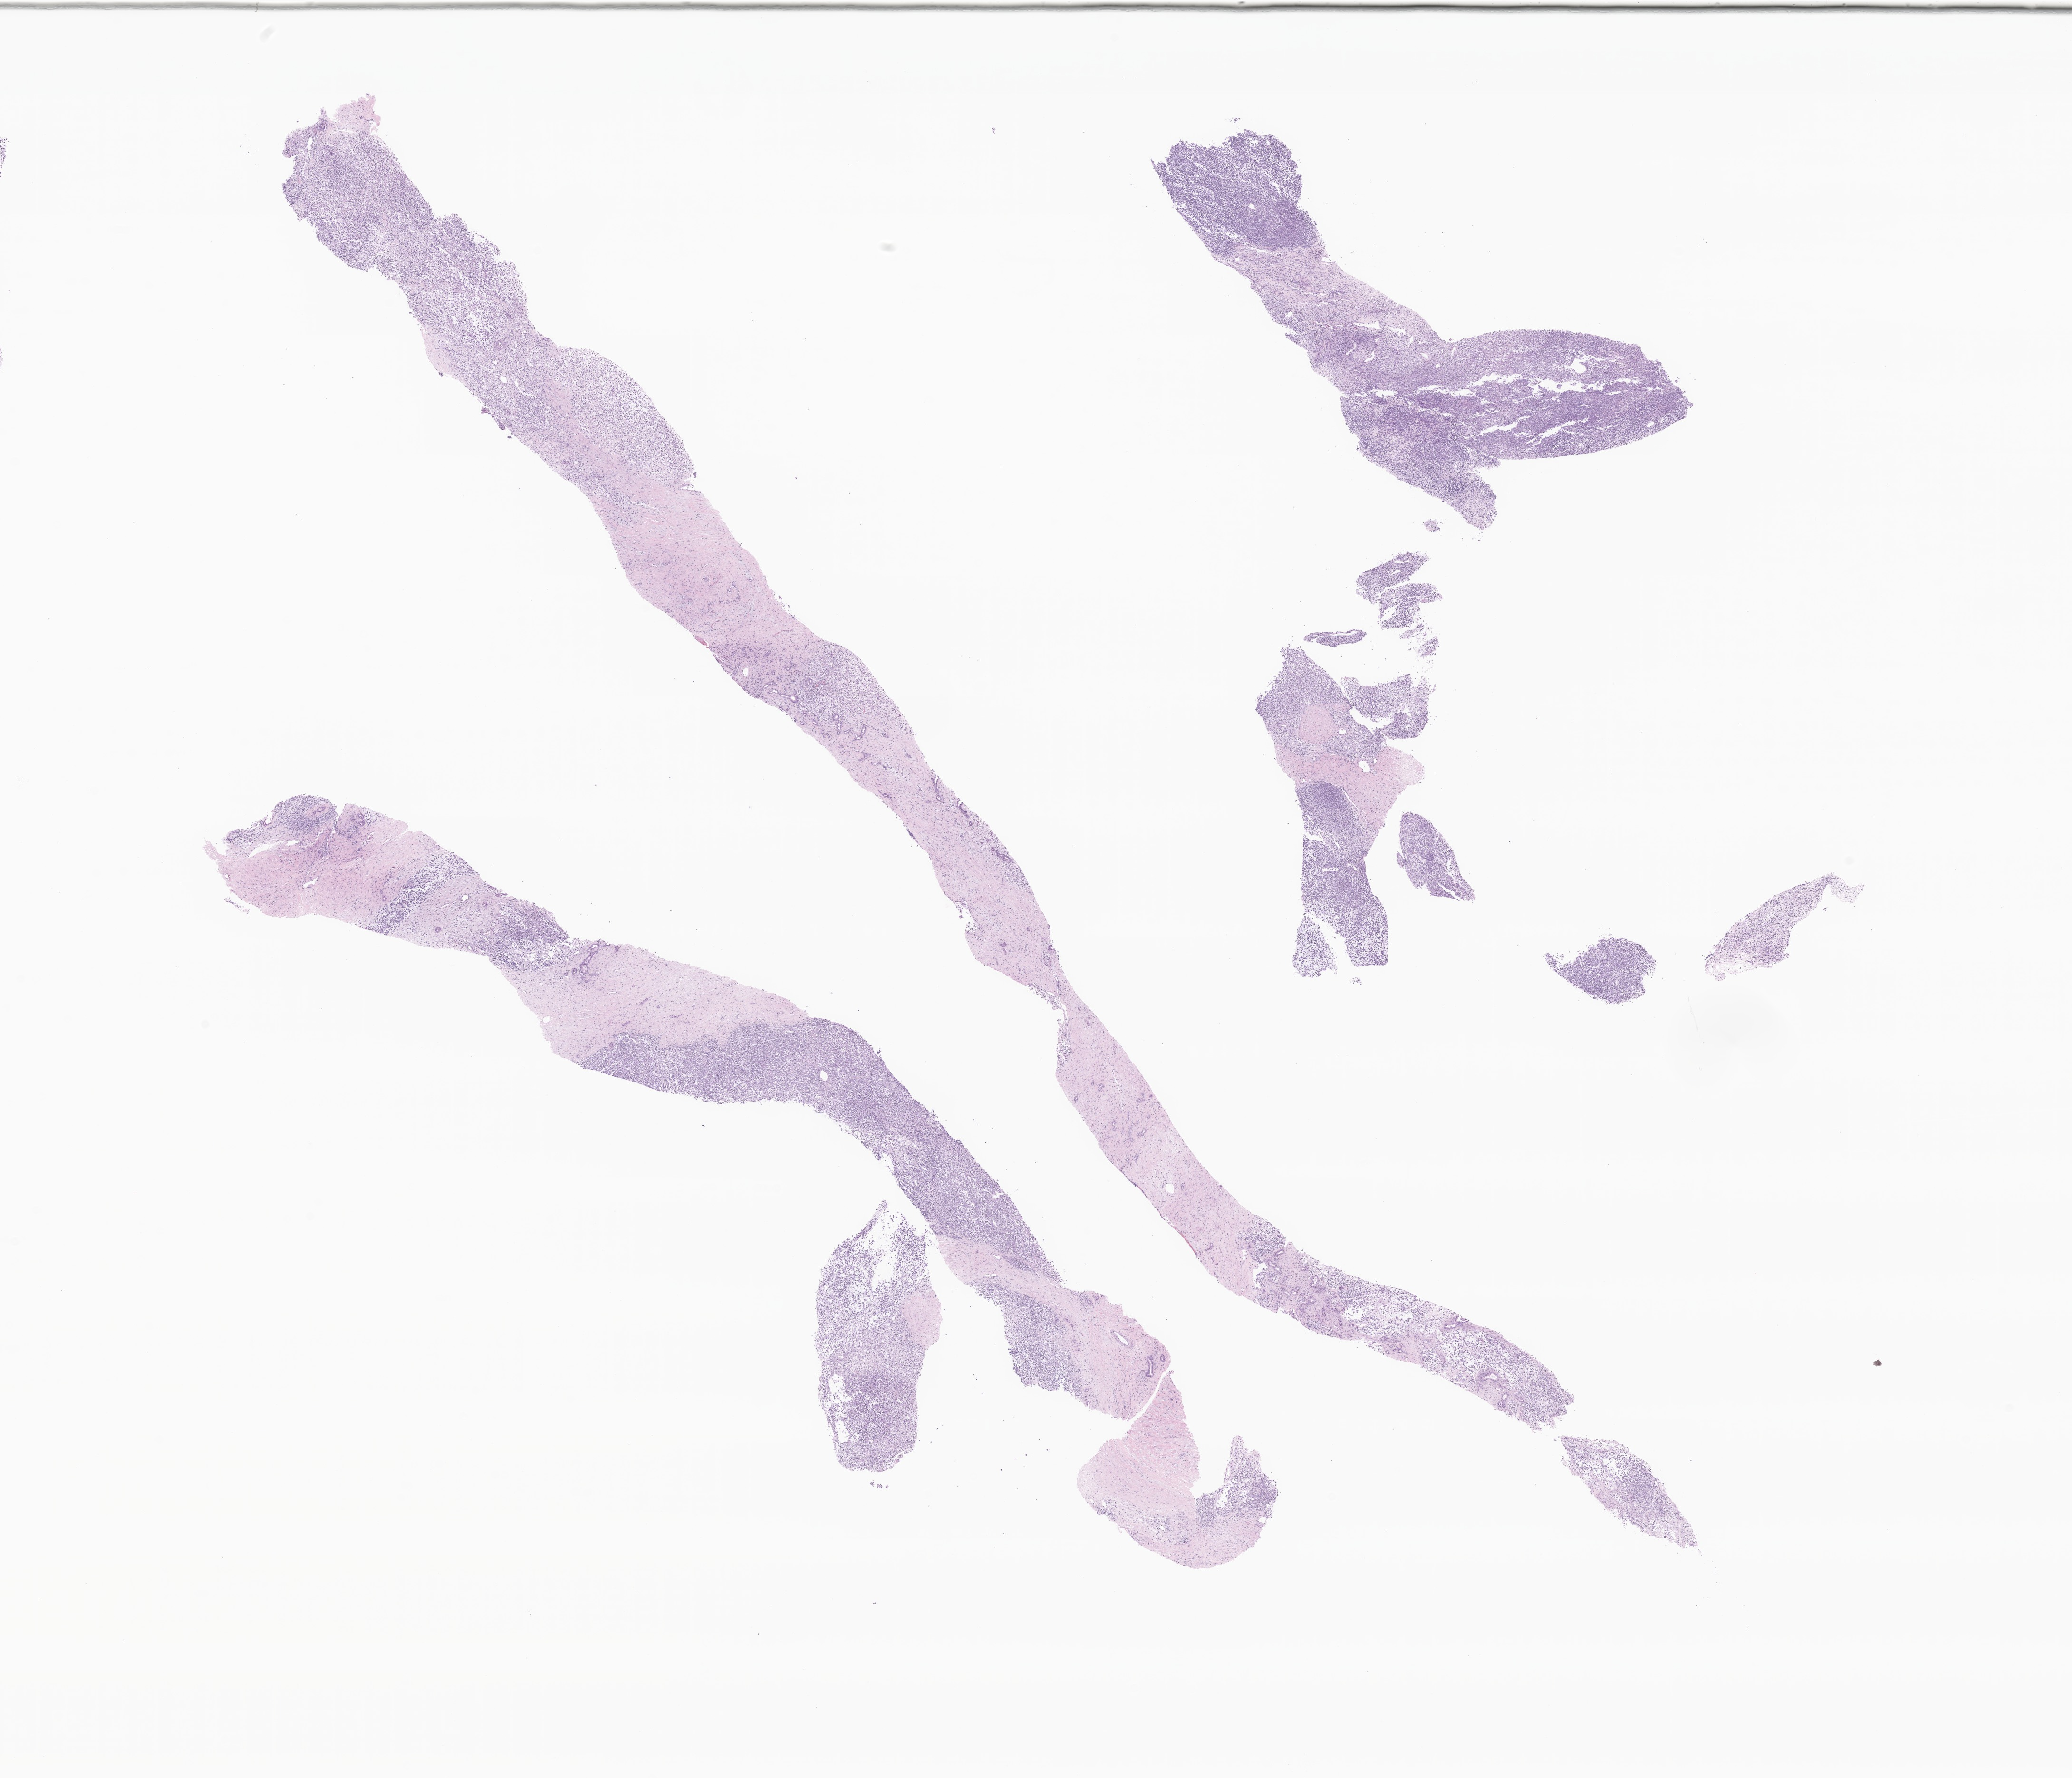
Hematoxylin and eosin (H&E) whole-slide image of tumor tissue from the liver — a low-resolution overview of the entire scanned area, about 18.4 x 15.8 mm; formalin-fixed paraffin-embedded section. Male patient, age 226 days.
• recorded diagnosis: Rhabdoid tumor, NOS